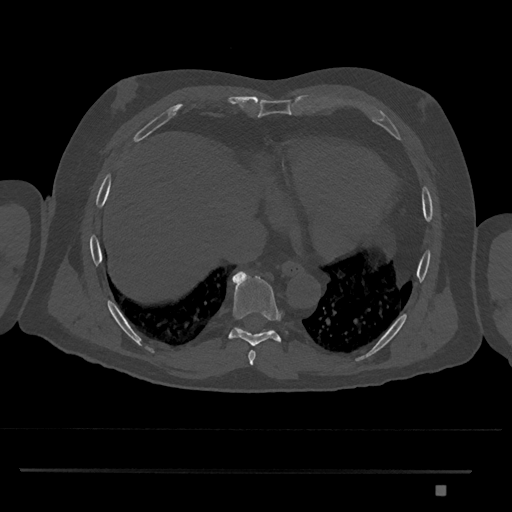
CT including the spine, one axial slice. Slice 1105 of 1134 in the series (ordered by position). 120 kVp. Bone window (W 1800 / L 400 HU). 0.5 mm slice thickness. 512 × 512 image matrix, field of view 429 × 429 mm. Male patient, age 65 years. Case-level facts recorded for this patient, not image findings: primary cancer: prostate.
Outlined on this slice (semi-automatic segmentation, software-assisted and operator-edited):
- T8 vertebra: bounding box [x1, y1, x2, y2] px = [229, 271, 282, 346]
- T9 vertebra: [237, 327, 272, 332]